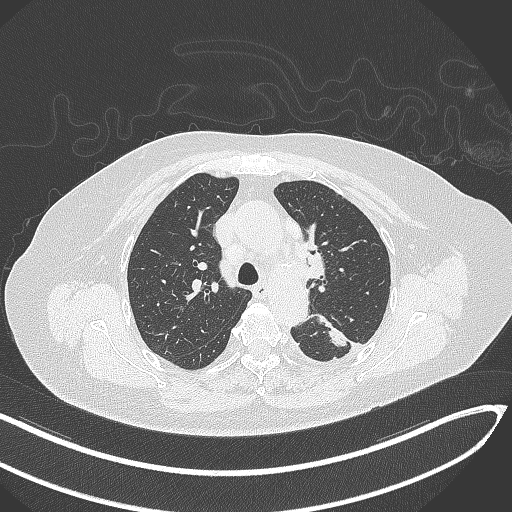
Chest CT, one axial slice. Position 220 of 270 along the scan axis. Reconstruction kernel B70f. 120 kVp. Lung window (W 1500 / L -600 HU). 512 × 512 image matrix, field of view 400 × 400 mm. Female patient, age 76 years. From the clinical record (not read from this slice): clinical TNM (as recorded): T1c N0 M0.
Outlined on this slice (bounding box drawn by a radiologist):
- lung tumour (recorded histology: adenocarcinoma): bounding box <309,315,348,353> (left, top, right, bottom; pixels)